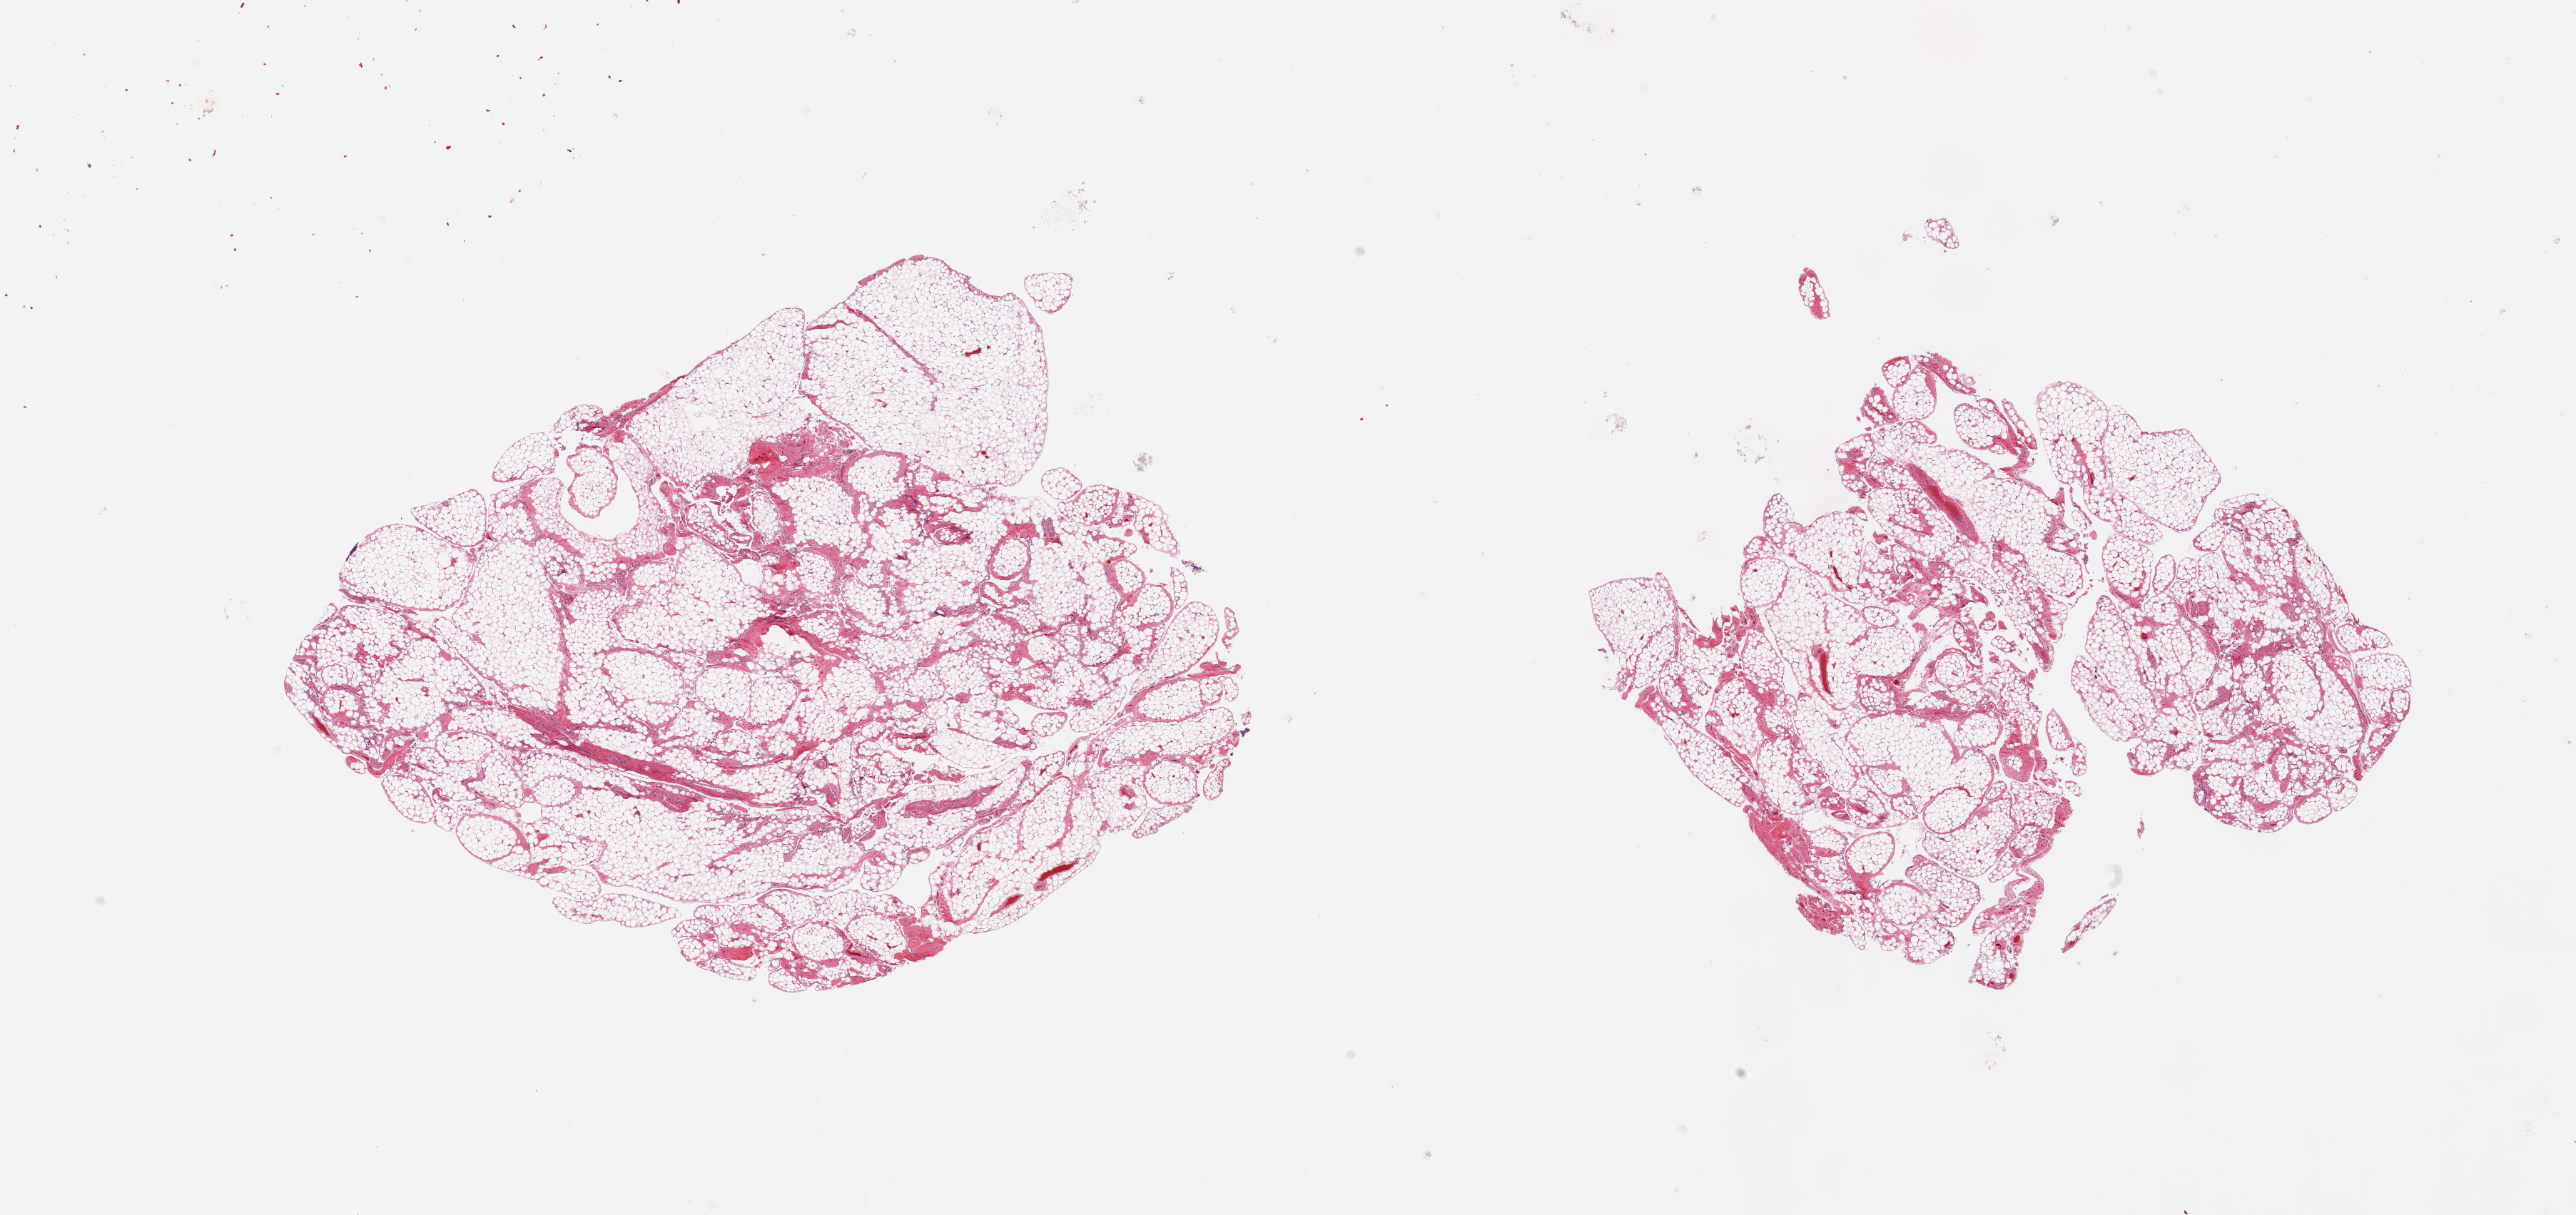
Whole-slide image, H&E stain — shown as a low-resolution overview of the whole scanned area (about 28.5 x 13.5 mm), PAXgene-fixed, paraffin-embedded tissue, sampled site (target tissue): omentum, tissue donor sample. Male donor.
Reviewer comment on this tissue sample: 2 pieces ~ 40% interstitial fibrosis/mesothelial hyperplasia.